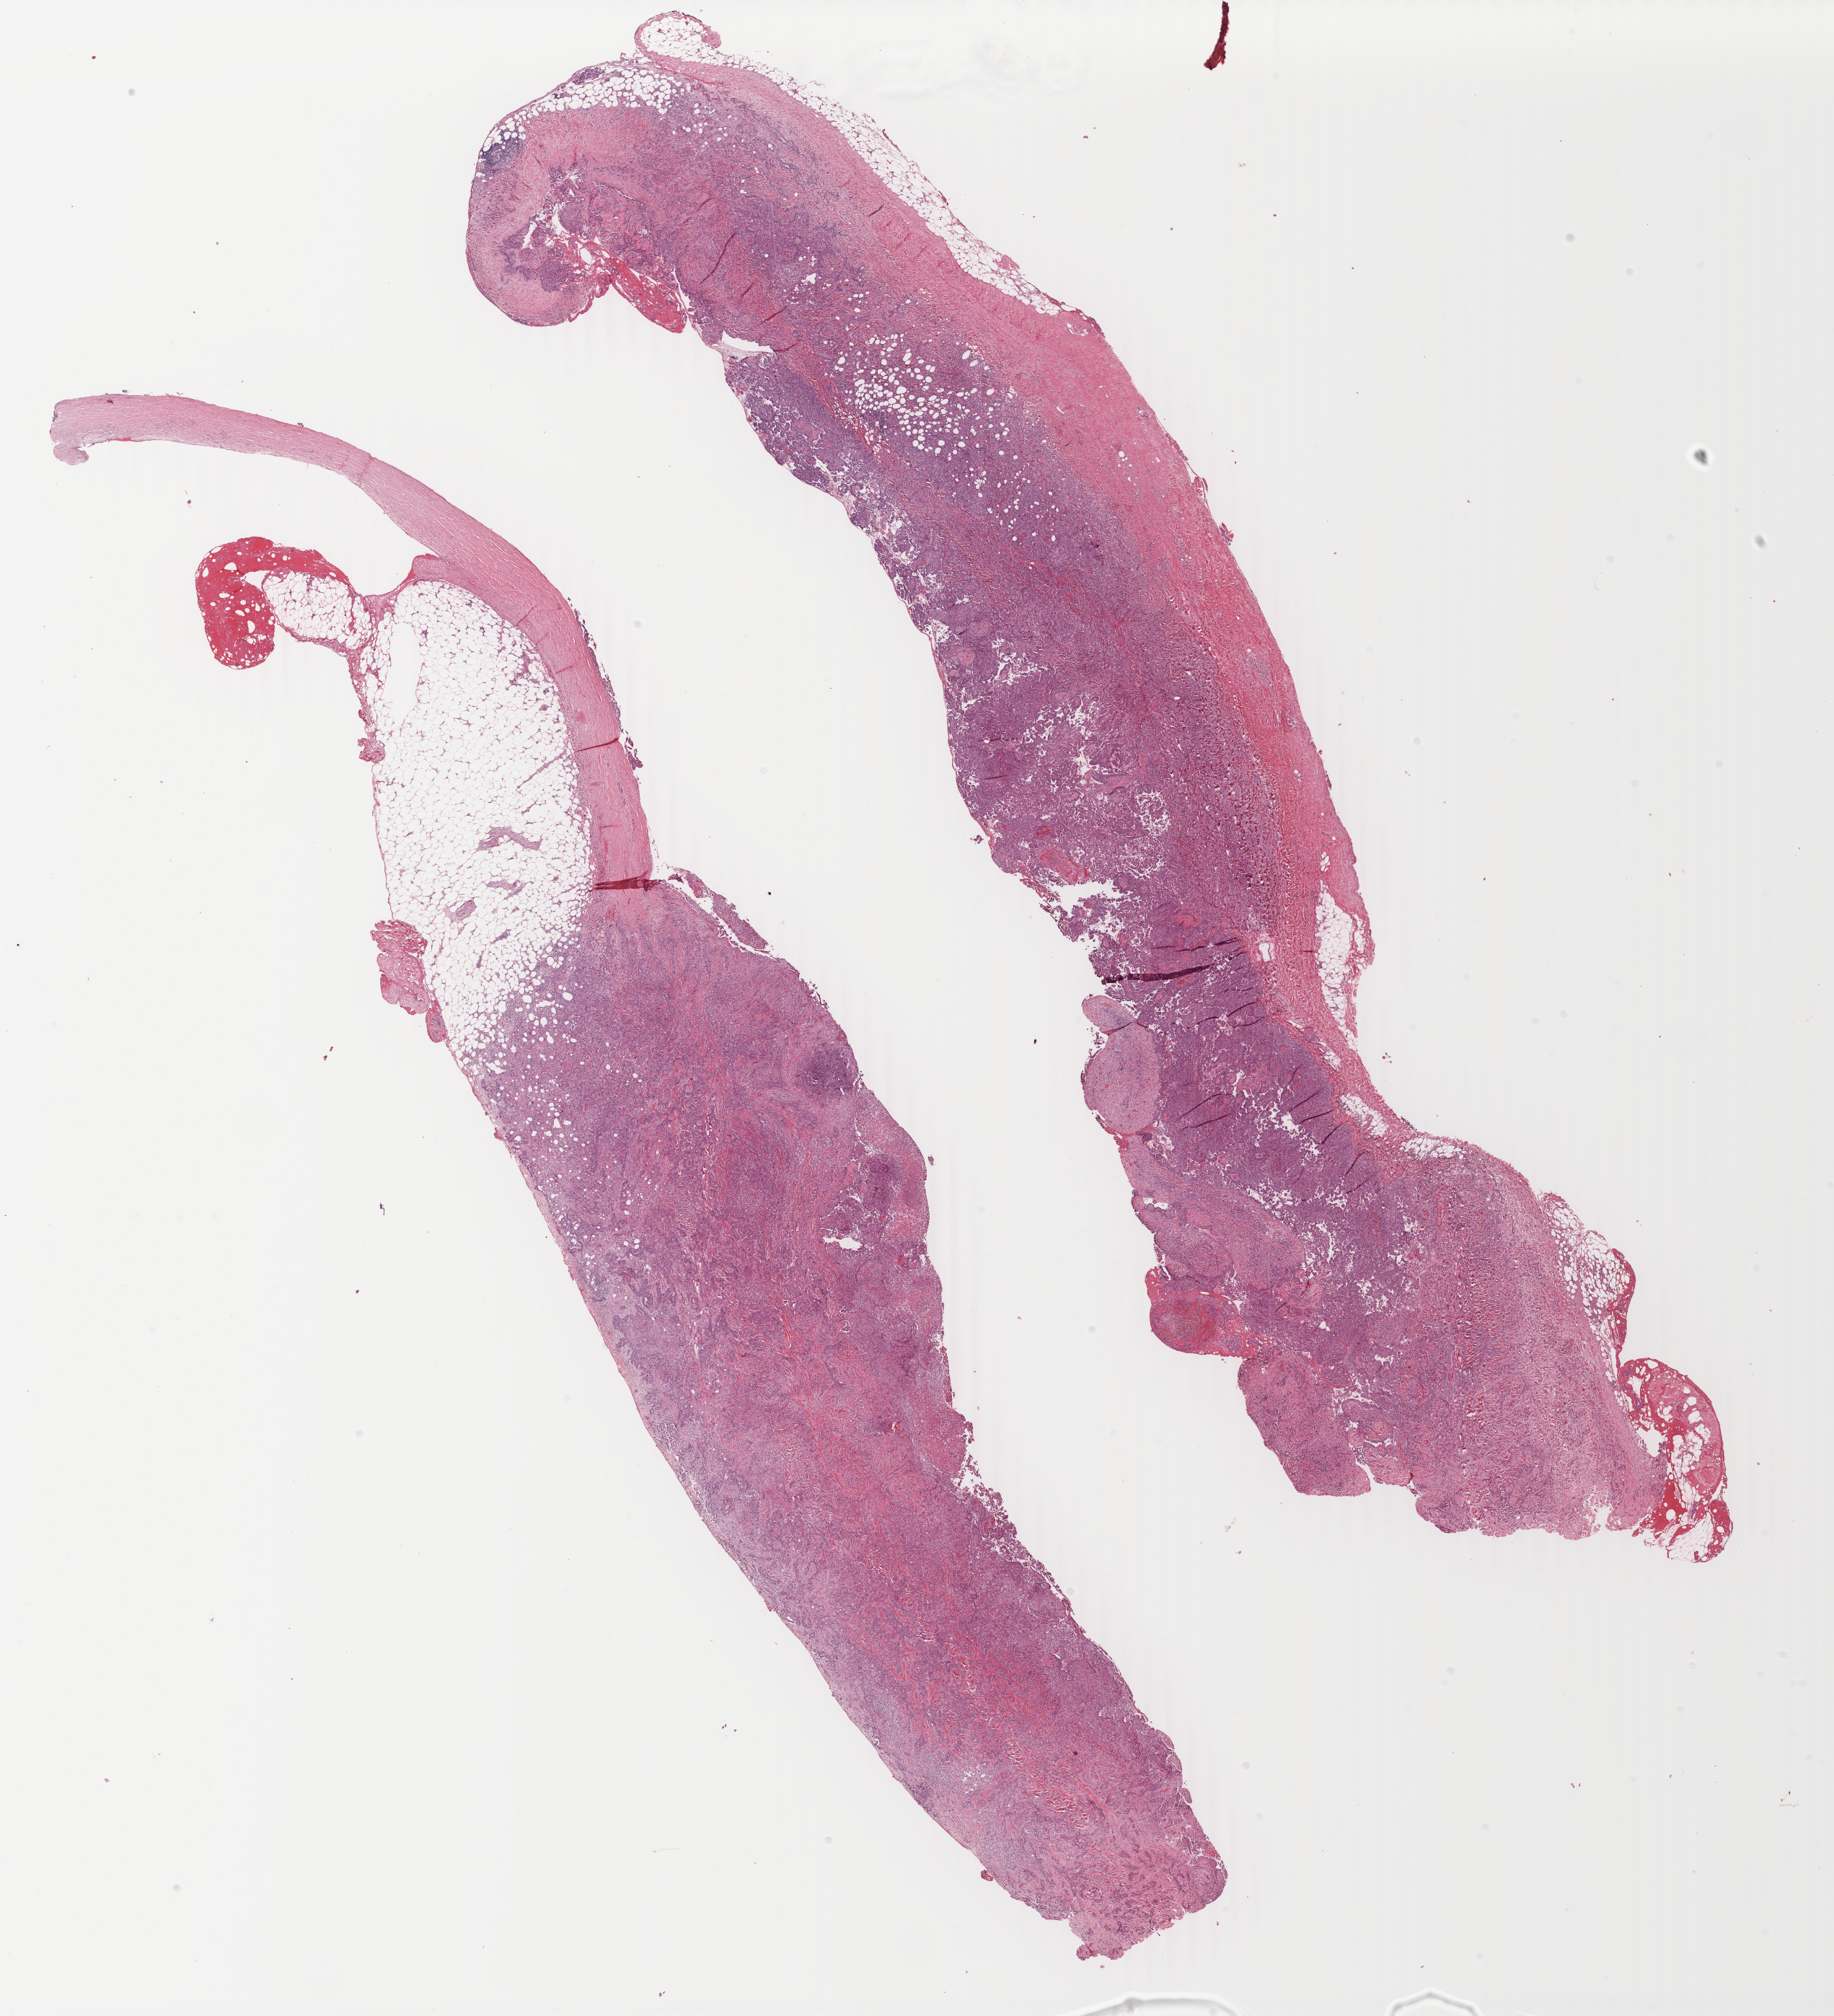
Whole-slide histology image, H&E, low-resolution overview of the scanned area, about 20.2 x 22.2 mm (slide scanned at 40x), FFPE section, primary tumour sample from the mesothelium. Male patient; age at initial diagnosis 64 years.
• AJCC pathologic stage: III (7th edition)
• diagnosis: Epithelioid mesothelioma, malignant (pleura, NOS)
• laterality: left